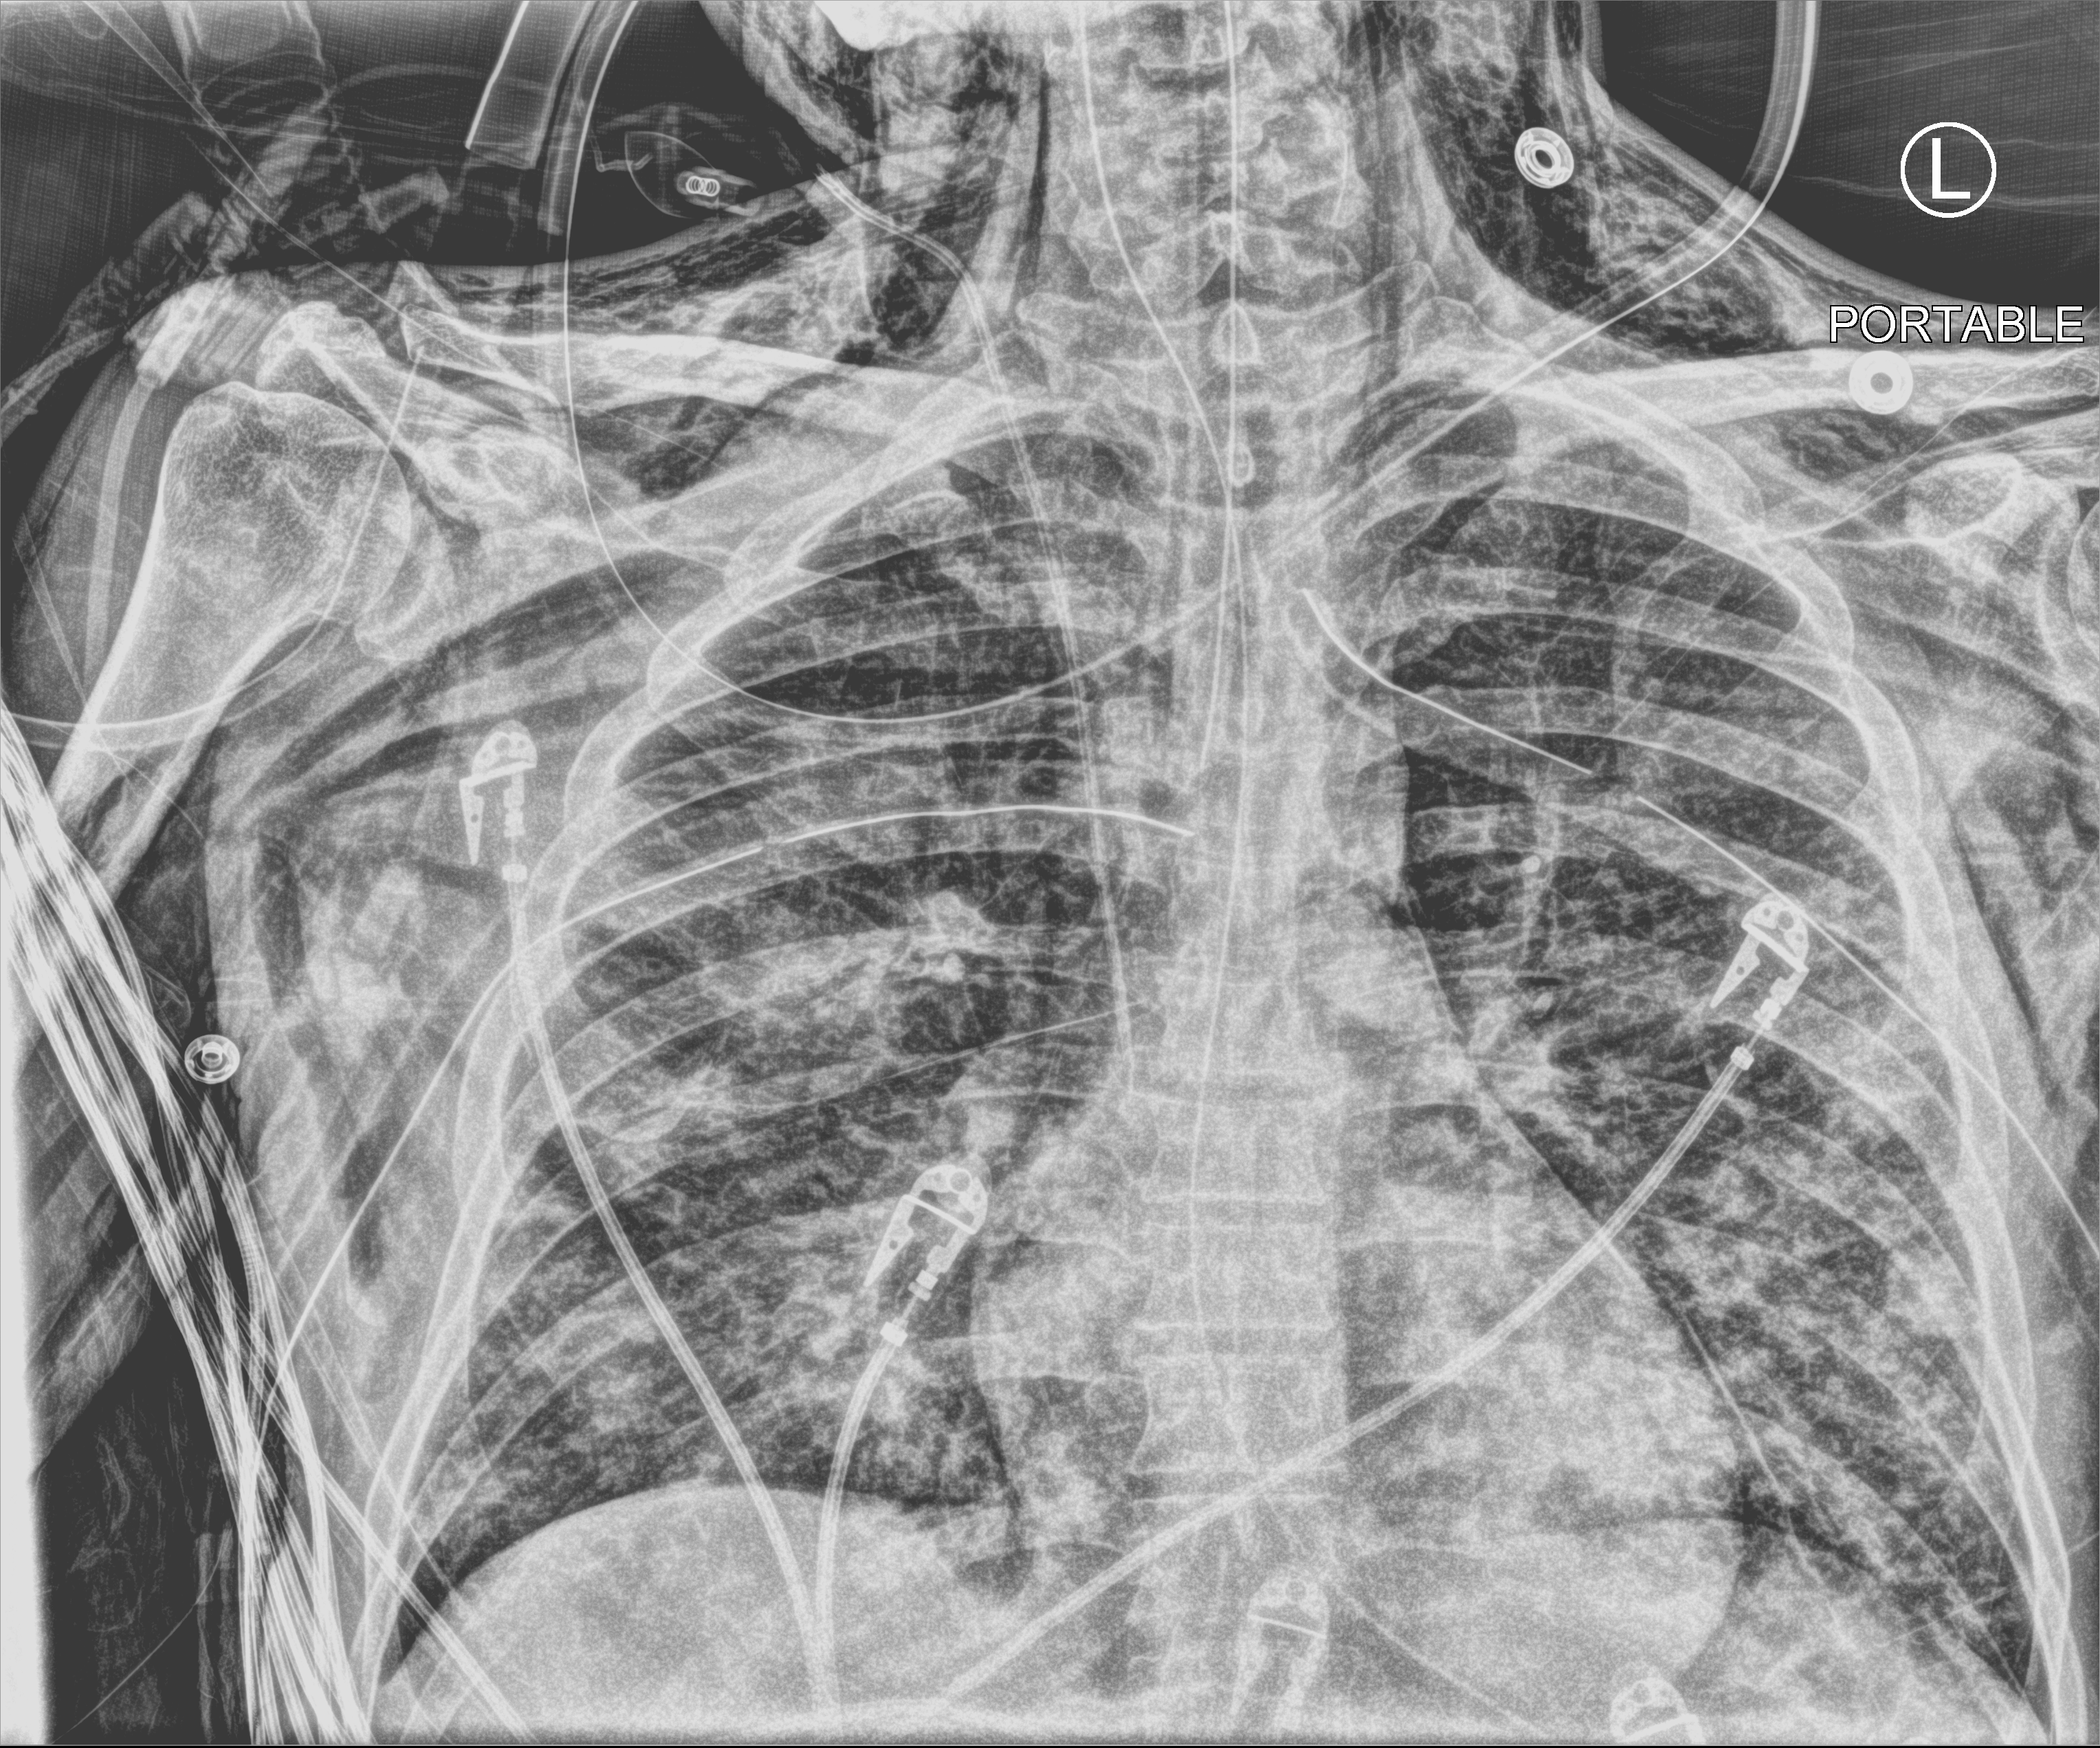
Chest X-ray (portable); anteroposterior (AP) projection. Patient hospitalised with COVID-19; male, aged 18–59 years.
Hospital-stay facts (about this admission, not read from this image; timing relative to this image not recorded): length of hospital stay: 96 days.